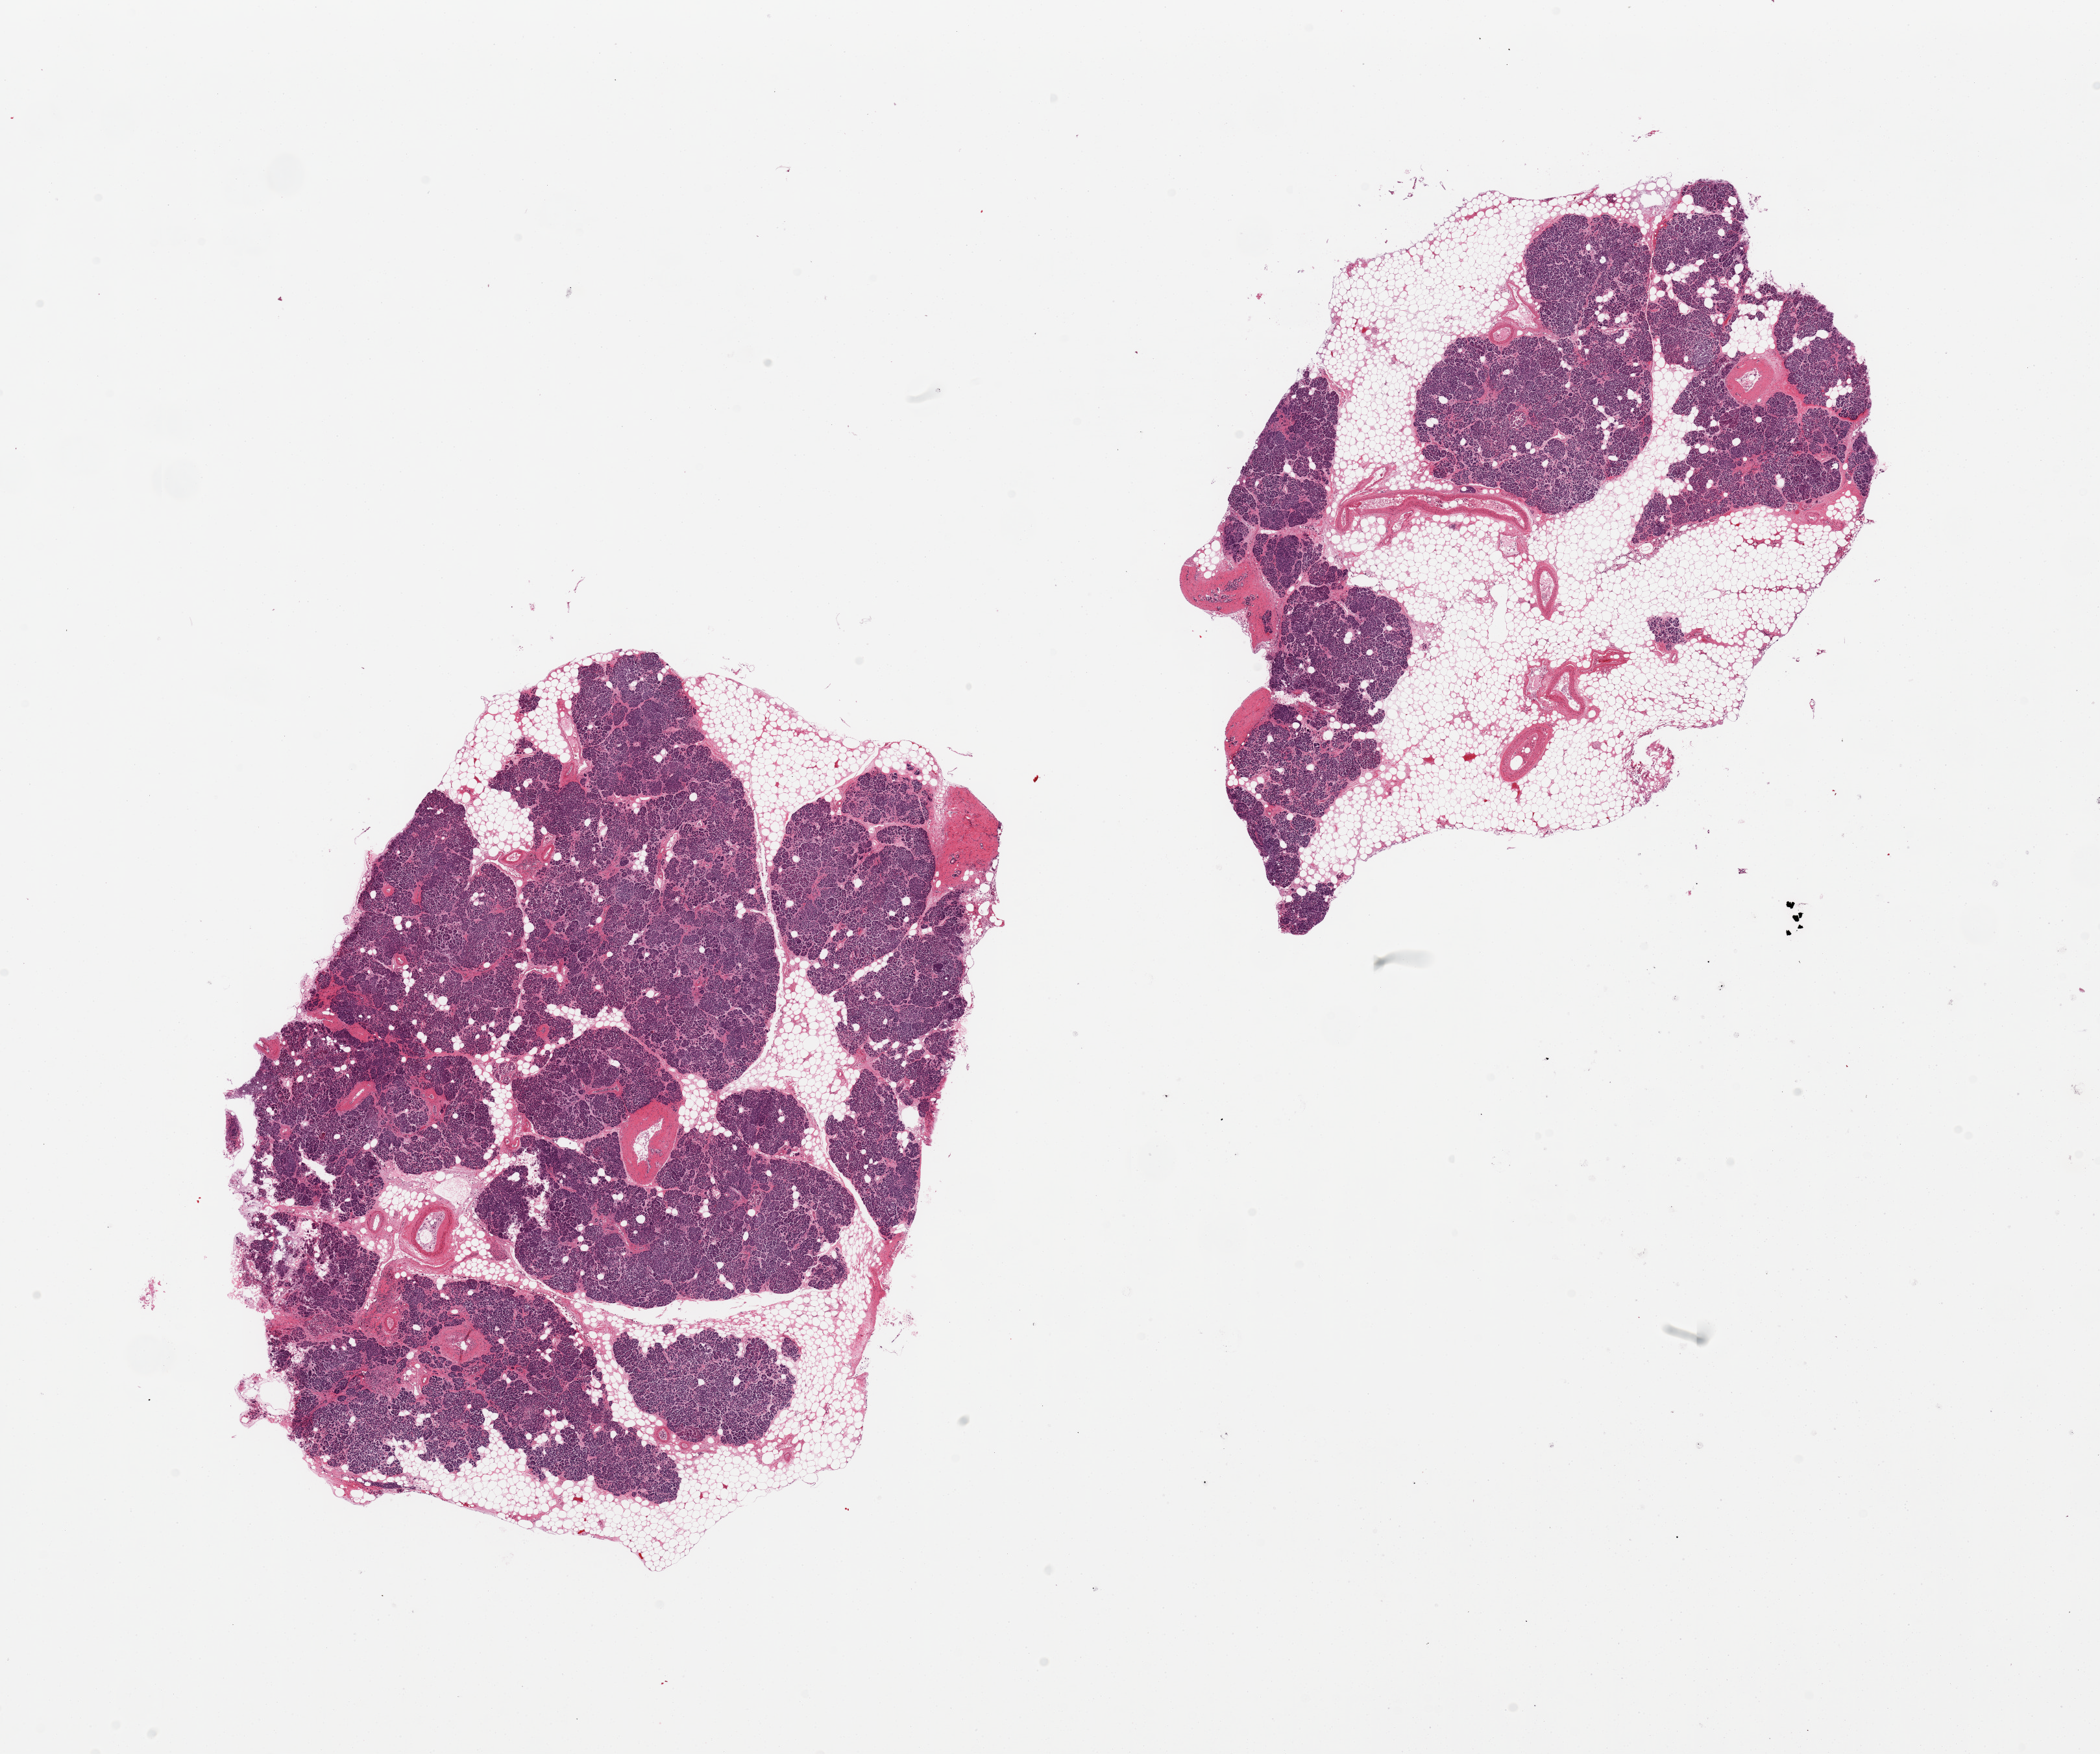
Digitized hematoxylin and eosin (H&E)-stained section, brightfield — a low-resolution overview of the entire scanned area, about 25.6 x 21.4 mm (acquisition: 20x scan); PAXgene-fixed, paraffin-embedded tissue; sampled site (target tissue): pancreas; donor tissue sample.
Review note (as recorded): 2 pieces; 10 and 50% fat.